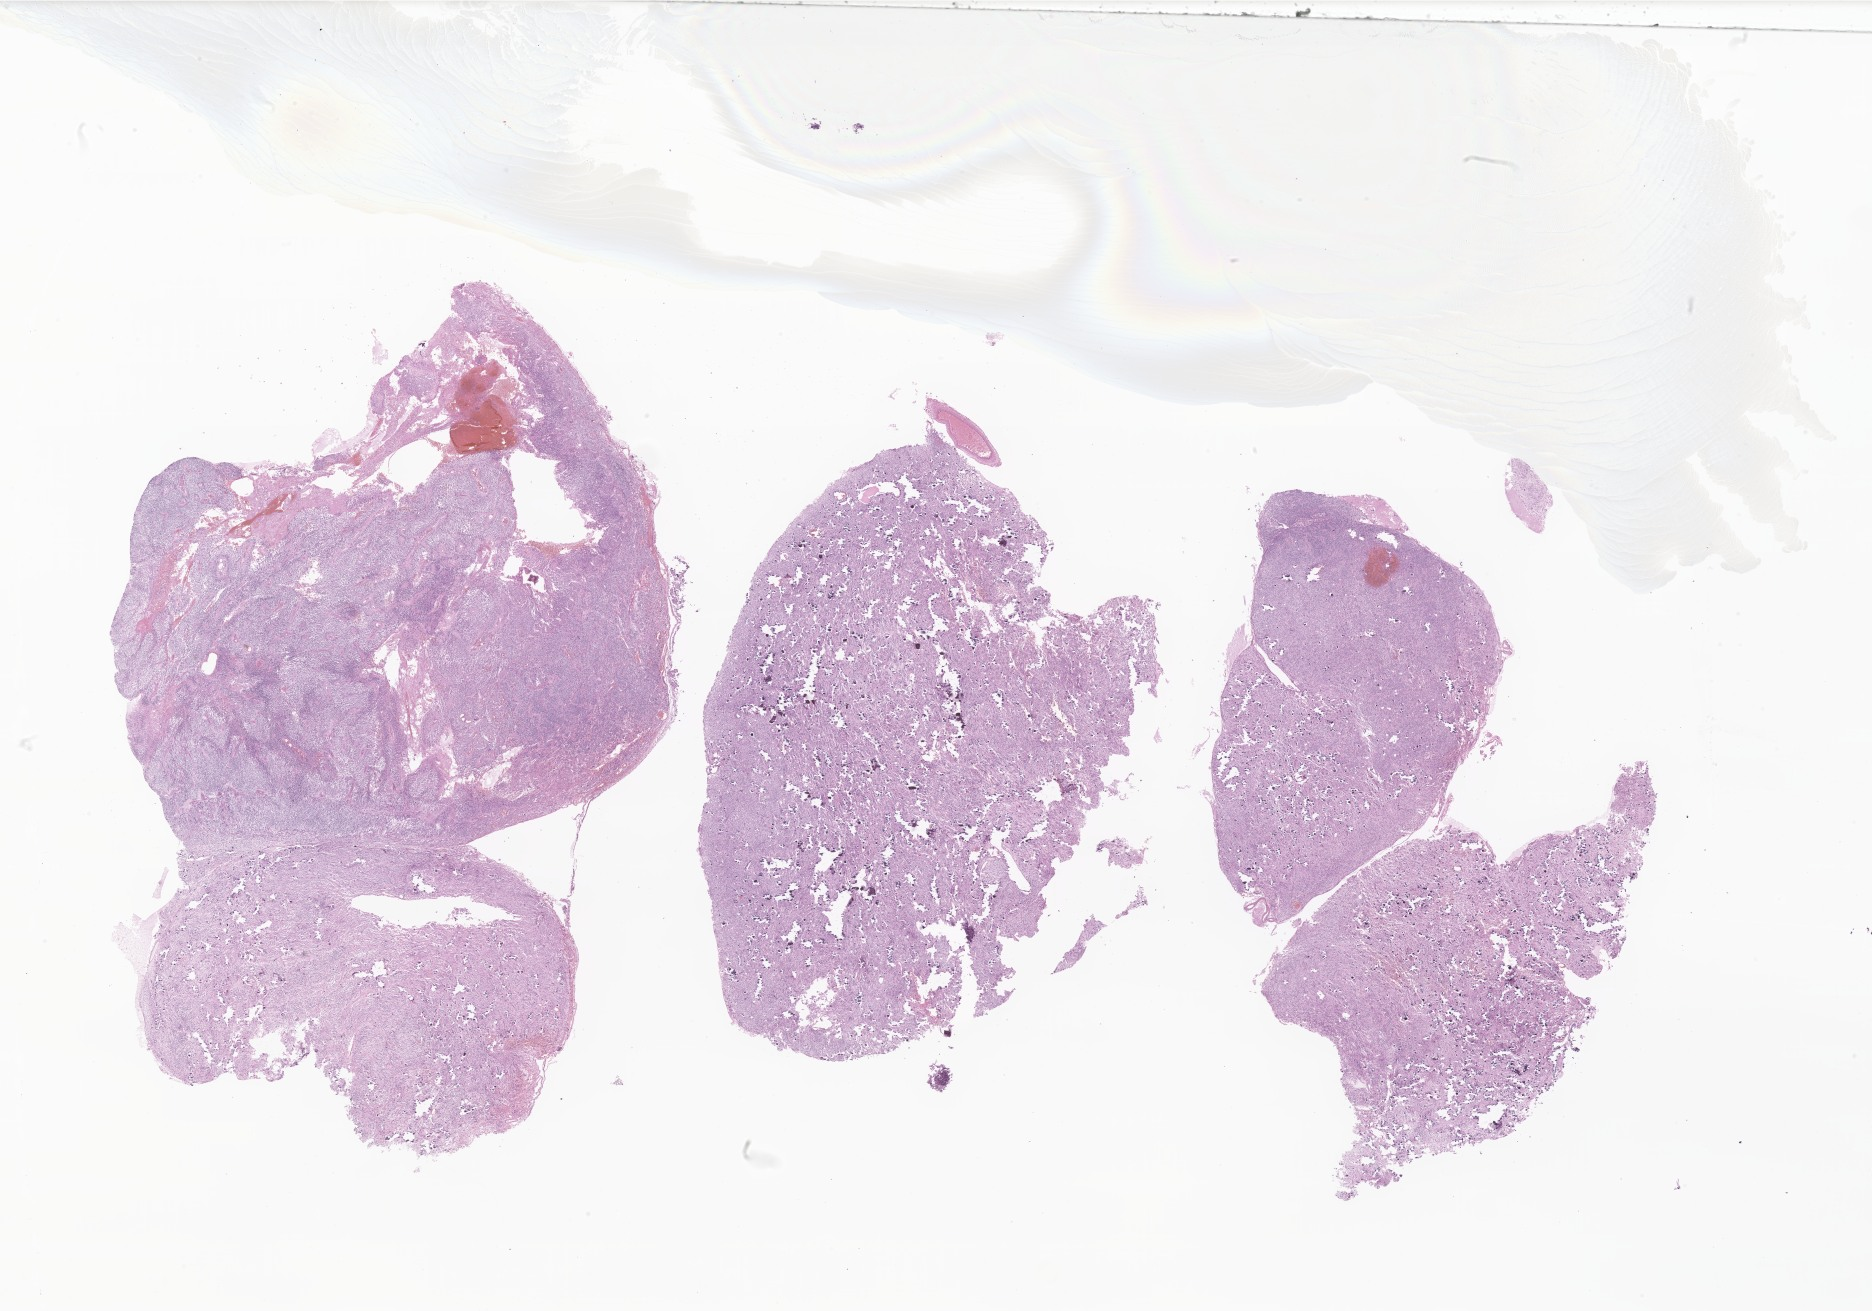
Digitized haematoxylin and eosin-stained section of tumor tissue from the occipital lobe — shown as a low-resolution overview of the whole scanned area (about 31.6 x 22.1 mm). FFPE section. Patient: male, age 102 months.
Recorded diagnosis: Ependymoma, NOS.